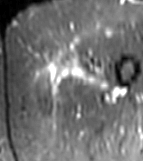
MRI of an extremity soft-tissue mass, one axial slice; position 9 of 81 along the scan axis; STIR; MR volume resampled by the dataset authors to the PET/CT grid (not the native acquisition matrix); 3.27 mm slice thickness; 143 × 161 image matrix, field of view 140 × 157 mm. Female patient. Case-level facts recorded for this patient, not image findings: histological type: myxofibrosarcoma; grade: intermediate; site of the primary tumour: left thigh.
Structures marked on this image (expert contour drawn on MRI and transferred to this co-registered scan by the dataset authors):
- gross tumour volume including surrounding oedema: bounding box [x1, y1, x2, y2] px = [40, 55, 109, 95]